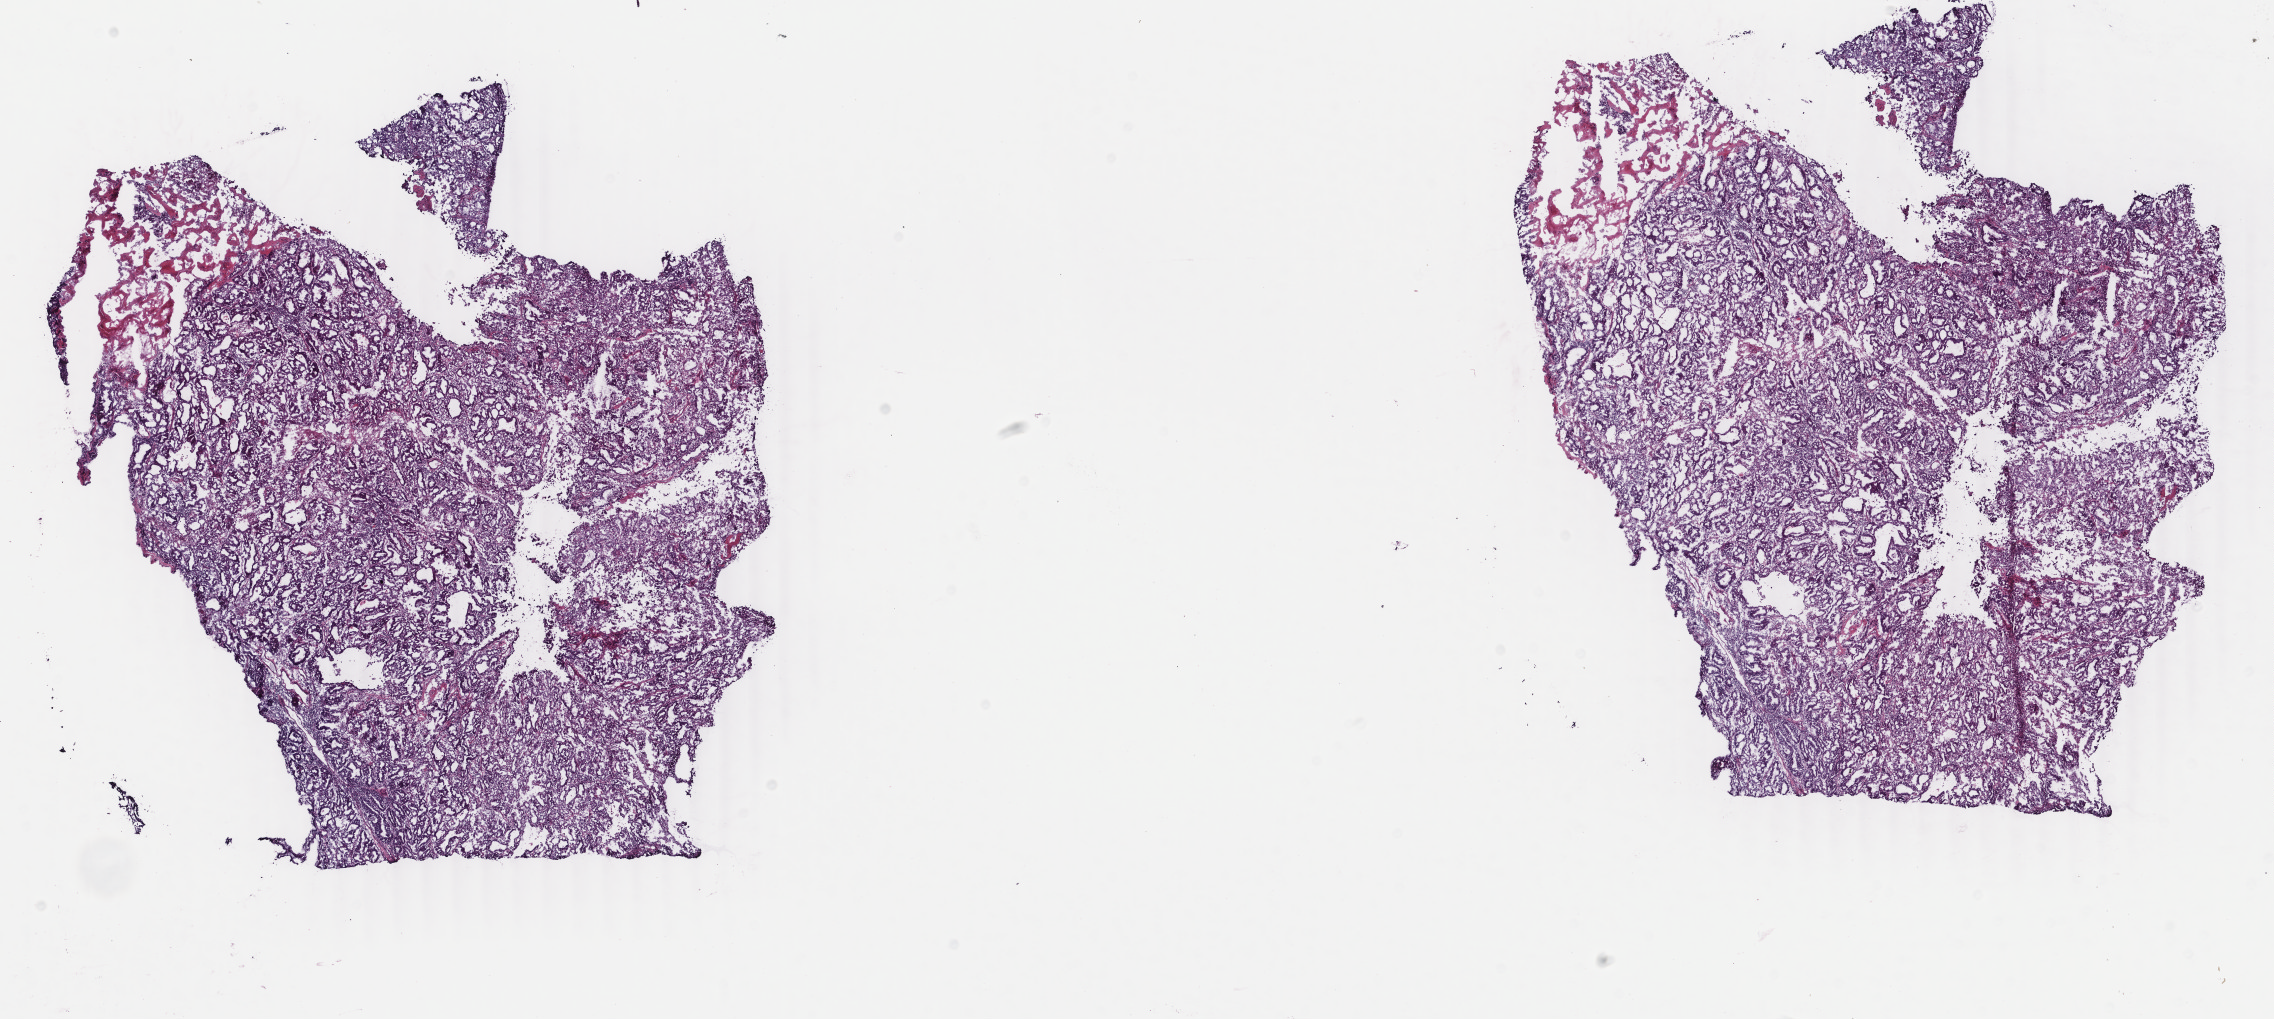
Digitized Hematoxylin and eosin (H&E) stained tissue section (whole slide), low-resolution overview of the scanned area, about 18.1 x 8.1 mm (slide scanned at 40x), frozen section, sample: primary tumour, uterus. Female patient; age at initial diagnosis 67 years. Histologic grade: G2 (moderately differentiated). Pathologist review of this section (percent, as recorded): tumour cells 85%, tumour nuclei 85%, normal cells 0%, stromal cells 5%, necrosis 10%. Inflammatory infiltration, as recorded: lymphocyte infiltration 5%, monocyte infiltration 10%, neutrophil infiltration 5%.
* FIGO stage: IIIA
* diagnosis: Endometrioid adenocarcinoma, NOS (endometrium)